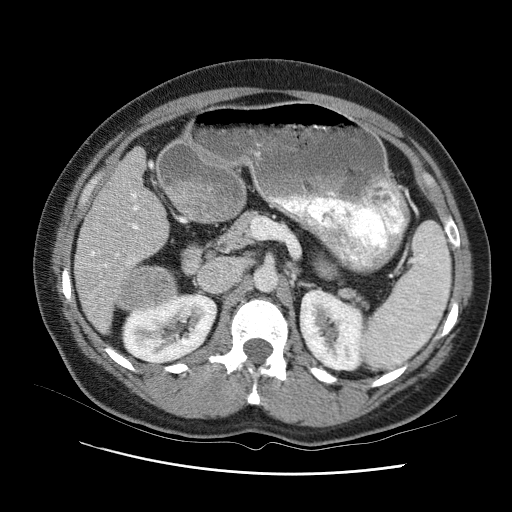
Contrast-enhanced abdominal CT (liver protocol), one axial slice; position 43 of 95 along the scan axis; 120 kVp; one of 2 acquisitions stored at this slice position; soft-tissue window (W 400 / L 40 HU); 2.5 mm slice thickness; 512 × 512 image matrix, field of view 360 × 360 mm. Case-level facts recorded for this patient, not image findings: diagnosis: hepatocellular carcinoma (patient treated with transarterial chemoembolisation; whether this scan precedes or follows treatment is not stated here); TNM stage (as recorded): Stage-I; Child-Pugh class: B; tumour differentiation: moderately differentiated; tumour nodularity: uninodular.
Outlined on this slice (semi-automatically segmented with operator editing):
- liver parenchyma outside the tumour (the mass and vessels are separate outlines, so this box may not span the whole liver): bounding box [x1, y1, x2, y2] px = [74, 138, 182, 344]
- mass: [115, 250, 184, 313]
- liver vessels: [96, 158, 161, 320]